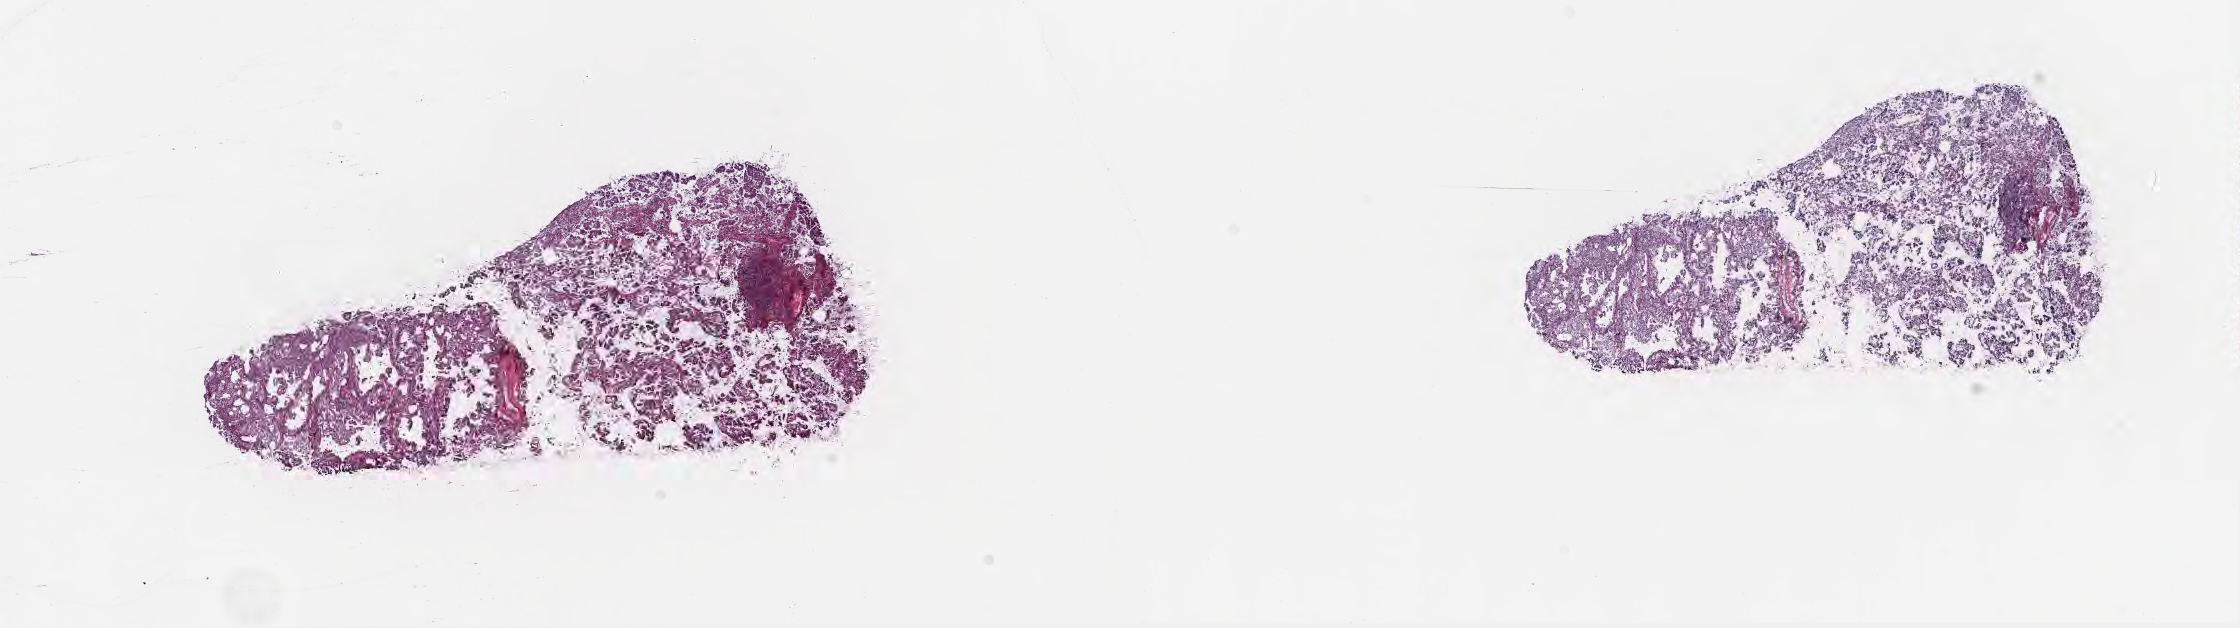
Haematoxylin and eosin whole-slide image — whole scanned area (about 18.1 x 5.1 mm) shown as a low-resolution overview; cryosection; specimen: primary tumor; anatomic site: lower lobe of right lung. Male patient, age 54 years. Slide review estimates, as recorded: tumor cells 90%, tumor nuclei 70%, stromal cells 0%, necrosis 0%, normal cells 10%. Infiltration values recorded for this section: lymphocyte infiltration 0%, monocyte infiltration 0%, neutrophil infiltration 0%.
AJCC pathologic stage: Stage IIA. Histologic diagnosis: Adenocarcinoma with mixed subtypes. Section: top of the tissue portion.